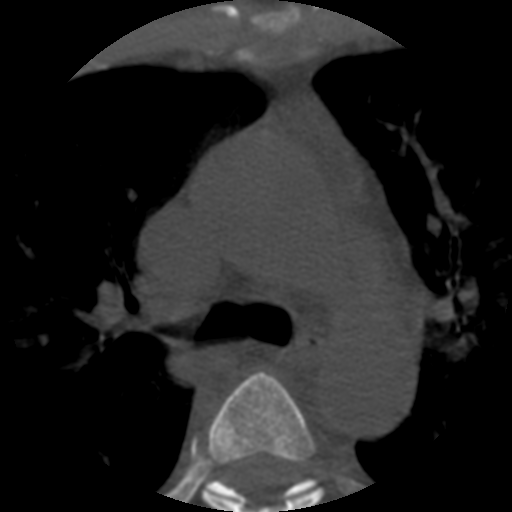
CT including the spine, one axial slice; slice 389 of 508 in the series (ordered by position); reconstruction kernel STANDARD; 120 kVp; bone window (W 1800 / L 400 HU); 1.25 mm slice thickness; 512 × 512 image matrix, field of view 160 × 160 mm. Patient age 57 years. From the clinical record (not read from this slice): primary cancer: prostate.
Outlined on this slice (semi-automatic segmentation, software-assisted and operator-edited):
- T4 vertebra: box from (x=202, y=371) to (x=323, y=512) px
- T5 vertebra: (x=205, y=478)–(x=317, y=501)